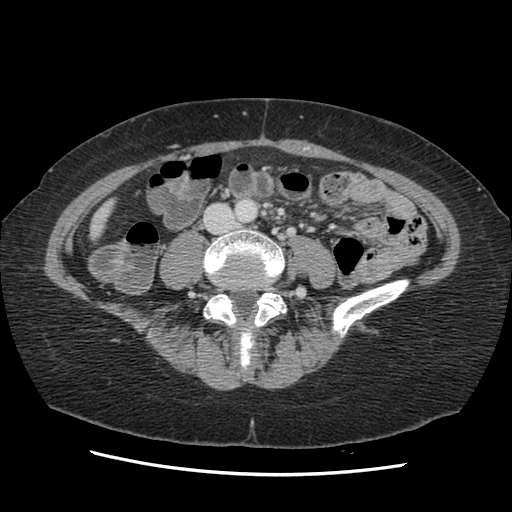
Contrast-enhanced abdominal CT, one axial slice. 120 kVp. Soft-tissue window (W 400 / L 40 HU). 2.5 mm slice thickness. 512 × 512 image matrix, field of view 330 × 330 mm. Female patient, age 61 years. Case-level facts recorded for this patient, not image findings: diagnosis: colorectal cancer liver metastases, imaged before liver resection; multiple liver metastases: no; largest metastasis: 2.4 cm; disease in both lobes: no.
Outlined on this slice (outlined manually by an expert reader):
- liver: bounding box <92,204,112,238> (left, top, right, bottom; pixels)
- planned liver remnant (the part of the liver to remain after resection): <92,204,112,238>